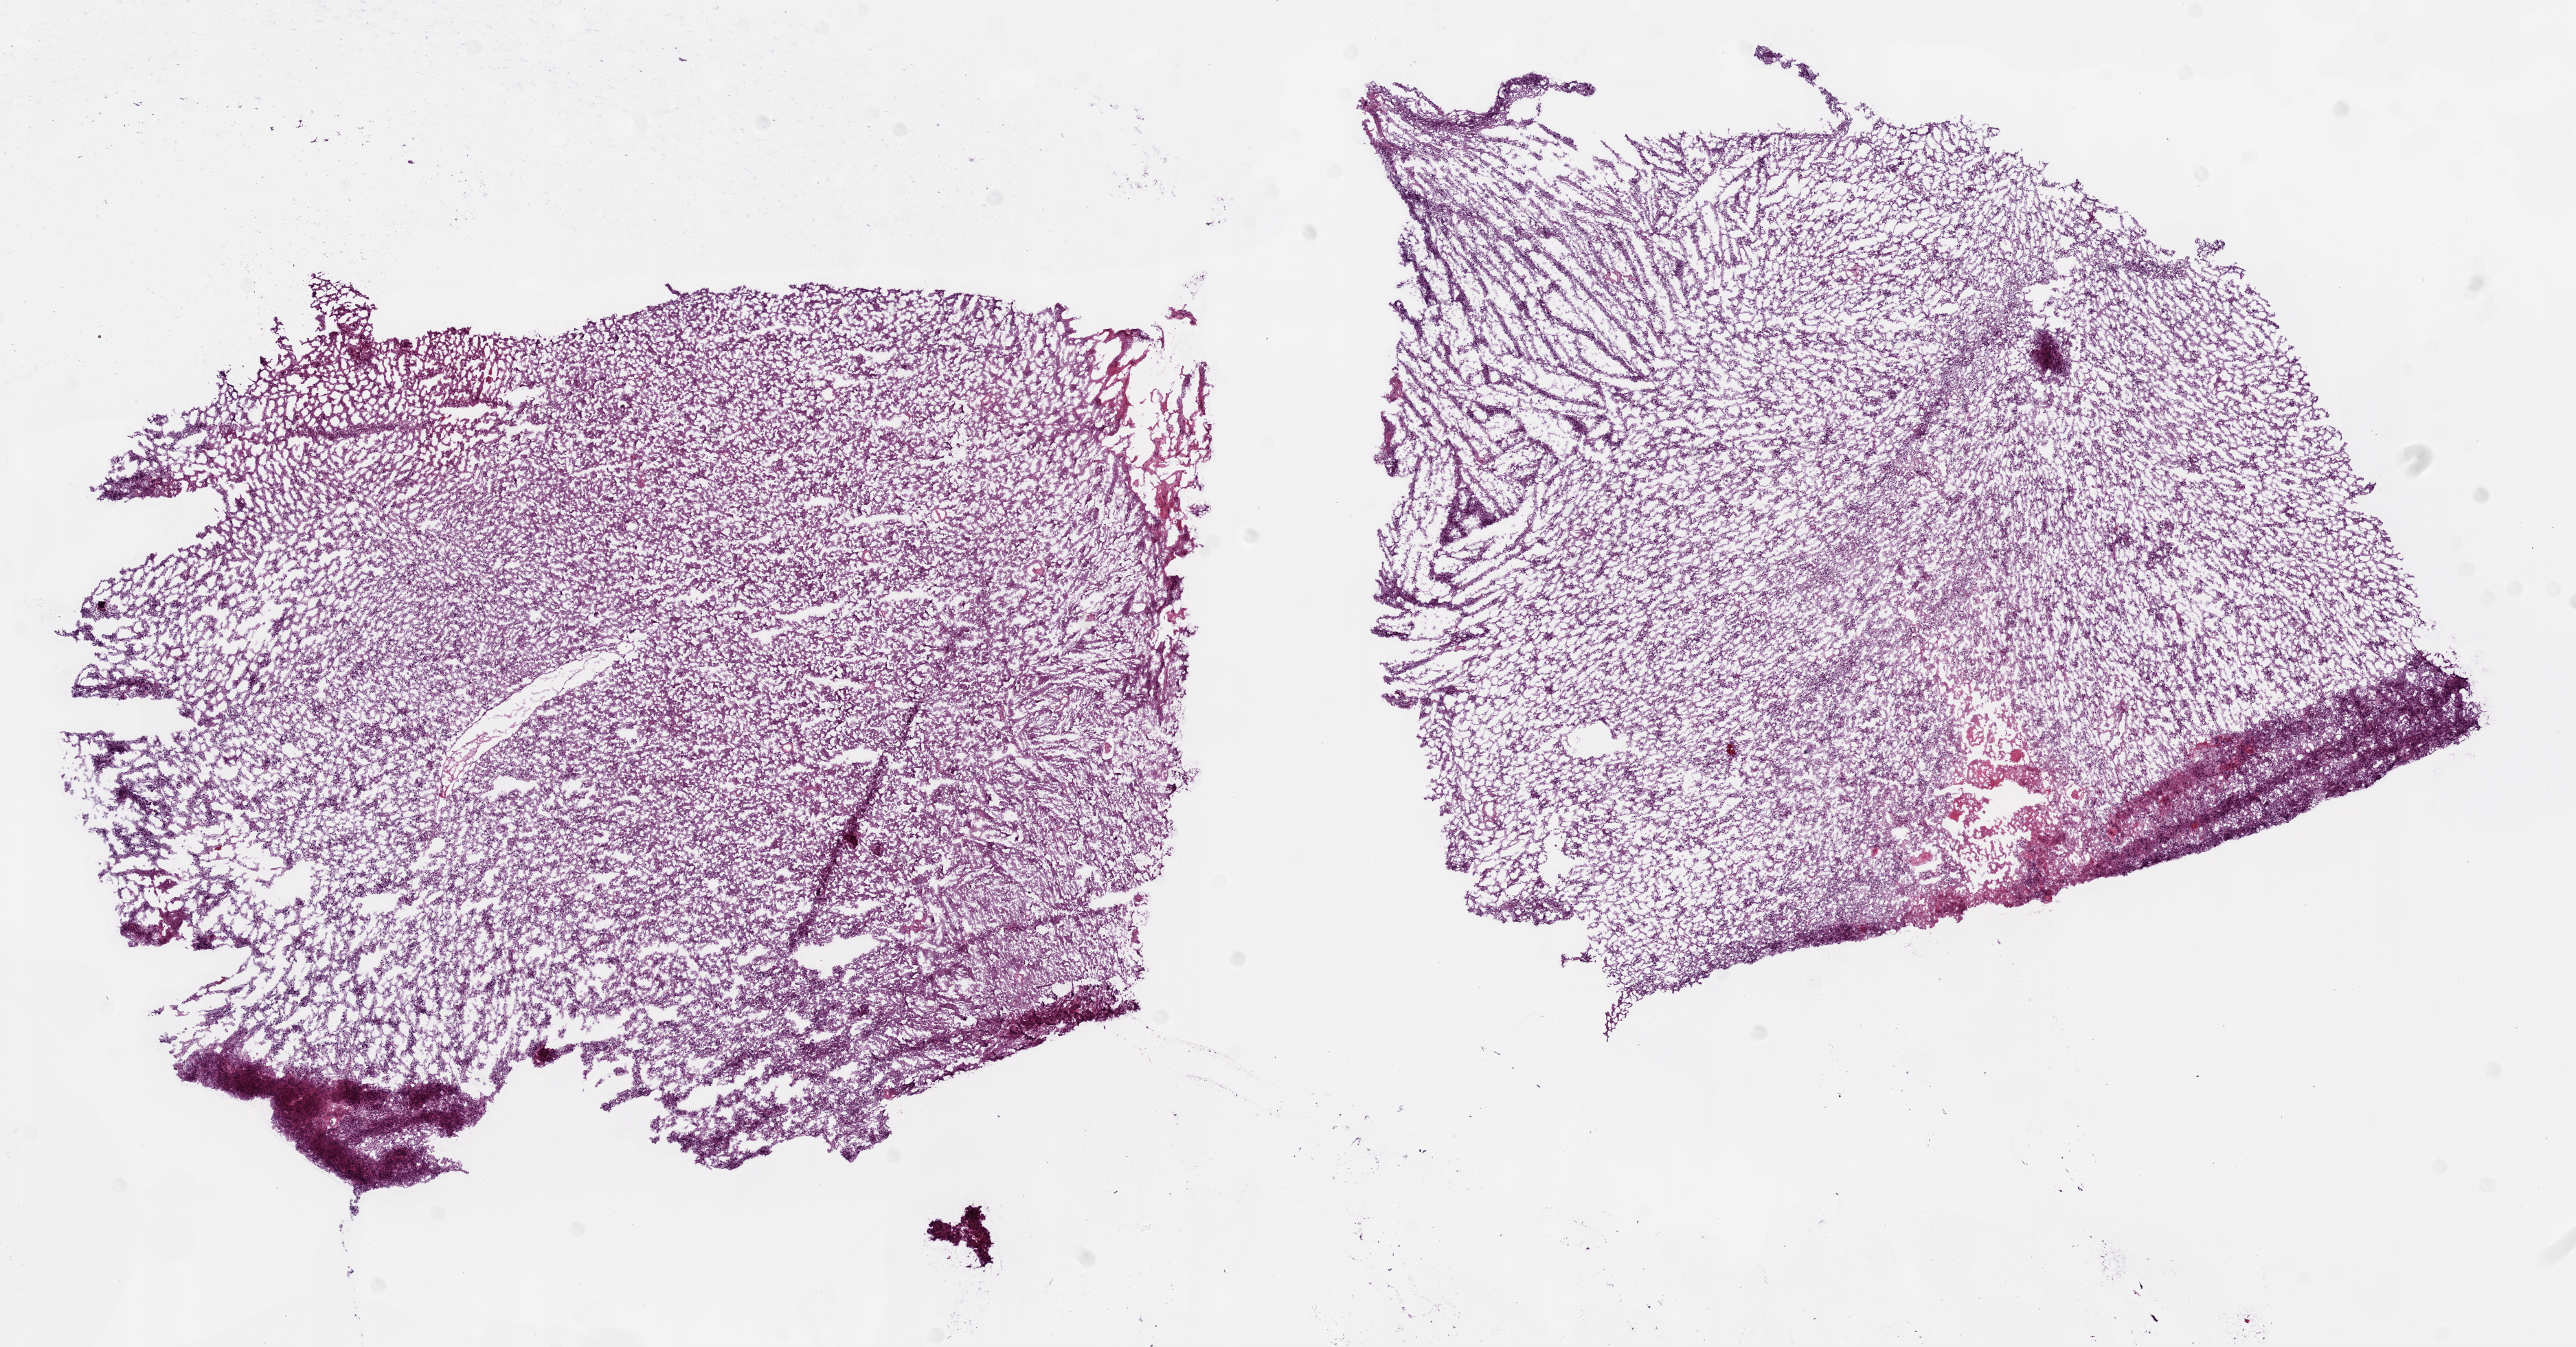
Whole-slide histology image, H&E-stained, whole scanned area (about 15.0 x 7.9 mm) shown as a low-resolution overview, frozen section, primary tumour sample from the brain. Male, age 68 years at initial diagnosis. Composition of this section per pathologist review: tumour cells 70%, tumour nuclei 80%, normal cells 20%, stromal cells 5%, necrosis 5%.
* pathologic diagnosis: Glioblastoma